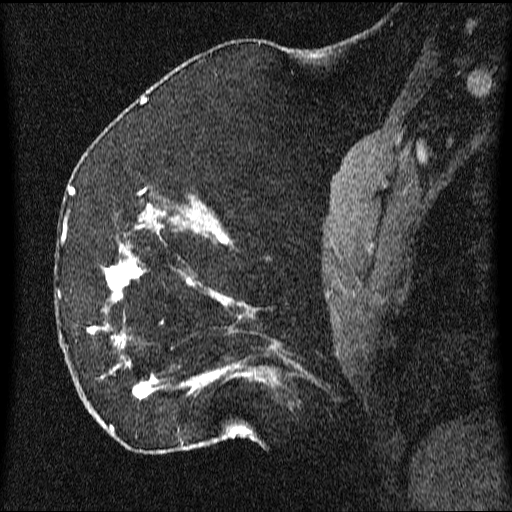
Breast MRI (dynamic contrast-enhanced), one sagittal slice. Slice 24 of 64 in the series (ordered by position). Dynamic contrast-enhanced series, image 2 of 3 at this slice position (ordered by acquisition). 1.5 T. TE 4.2 ms, TR 9.1 ms. 512 × 512 image matrix, field of view 180 × 180 mm. Female patient, age 52 years.
Structures marked on this image (semi-automatically segmented with operator editing):
- analysis volume of interest (the breast-tissue region the enhancement analysis was run in; not a lesion): bounding box (x1, y1, x2, y2) in pixels: (61, 203, 350, 438)
- tumour enhancement mask (voxels above the 70 % enhancement threshold inside the analysis volume of interest): (65, 203, 264, 431)